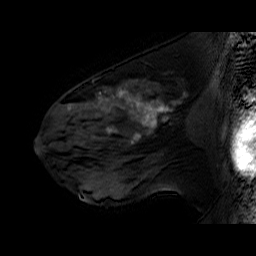
Breast MRI (dynamic contrast-enhanced), one sagittal slice; slice 33 of 60 in the series (ordered by position); dynamic contrast-enhanced series, time point 2 of 6 at this slice position (early post-contrast); 1.5 T; TE 6.4 ms, TR 32.9 ms; 4 mm slice thickness; 256 × 256 image matrix. Female patient. Case-level facts recorded for this patient, not image findings: setting: breast cancer imaged before/during neoadjuvant chemotherapy; receptor status: HER2-positive.
Structures marked on this image (semi-automatic segmentation, software-assisted and operator-edited):
- analysis volume of interest (the breast-tissue region the enhancement analysis was run in; not a lesion): bounding box (x1, y1, x2, y2) in pixels: (51, 78, 196, 160)
- tumour enhancement mask (voxels above the 100 % enhancement threshold inside the analysis volume of interest): (68, 88, 170, 143)